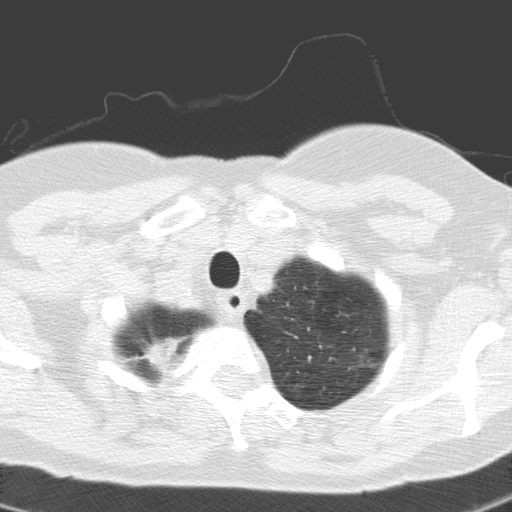
Axial slice from a low-dose chest CT screening exam. Baseline annual screen. Lung window (W 1500 / L -600 HU). Female participant, aged 60 years at enrolment.
Expert reader's lesion annotation, bounding box <114,316,198,384> (left, top, right, bottom; pixels). Screening reader's record for this exam: no non-calcified nodule ≥4 mm recorded. Lung cancer was diagnosed 391 days after this screen (after the second annual screen): squamous cell carcinoma, keratinizing, NOS, right upper lobe, moderately differentiated (G2), stage IA (AJCC 6th edition), 20 mm at pathology.